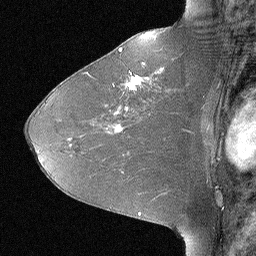
Breast MRI (dynamic contrast-enhanced), one sagittal slice. Position 39 of 64 along the scan axis. Dynamic contrast-enhanced study with each time point stored as its own series, time point 2 of 3 at this slice position (early post-contrast, ordered by acquisition time). 1.5 T. TE 4 ms, TR 30 ms. 2.25 mm slice thickness. 256 × 256 image matrix, field of view 180 × 180 mm. Female patient, age 46 years. Case-level facts recorded for this patient, not image findings: setting: breast cancer imaged before/during neoadjuvant chemotherapy; receptor status: HR-positive, HER2-negative.
Structures marked on this image (semi-automatically segmented with operator editing):
- analysis volume of interest (the breast-tissue region the enhancement analysis was run in; not a lesion): box from (x=106, y=43) to (x=184, y=119) px
- tumour enhancement mask (voxels above the 90 % enhancement threshold inside the analysis volume of interest): (x=119, y=48)–(x=161, y=89)